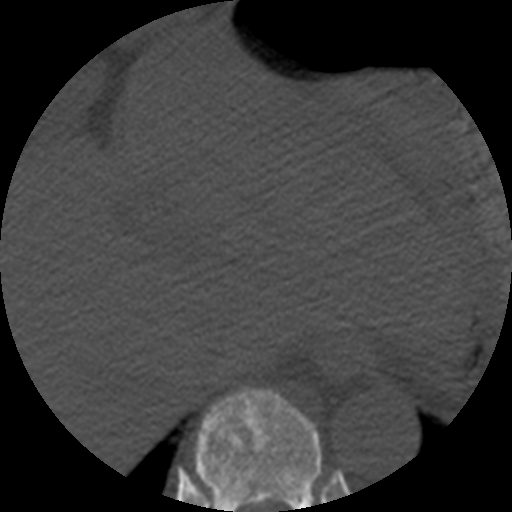
CT including the spine, one axial slice; slice 274 of 508 in the series (ordered by position); 120 kVp; bone window (W 1800 / L 400 HU); 1.25 mm slice thickness; 512 × 512 image matrix, field of view 160 × 160 mm. Patient age 57 years. From the clinical record (not read from this slice): primary cancer: prostate.
Annotated regions visible in this slice (semi-automatically segmented with operator editing):
- T10 vertebra: bounding box (x1, y1, x2, y2) in pixels: (195, 386, 322, 512)